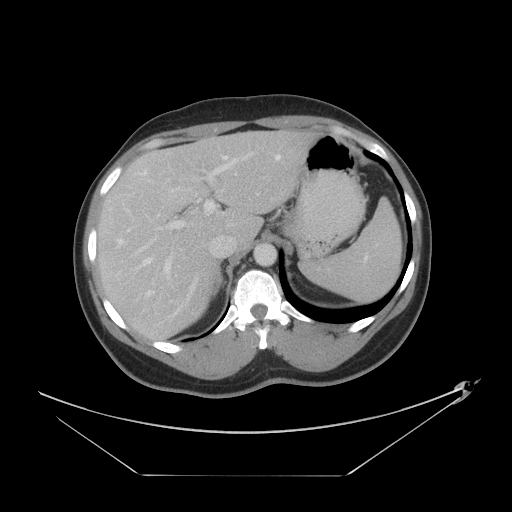
Contrast-enhanced abdominal CT, one axial slice. Position 29 of 44 along the scan axis. 120 kVp. Intravenous contrast given. Soft-tissue window (W 400 / L 40 HU). 512 × 512 image matrix, field of view 466 × 466 mm. Male patient, age 49 years. Case-level facts recorded for this patient, not image findings: diagnosis: colorectal cancer liver metastases, imaged before liver resection; multiple liver metastases: no; largest metastasis: 8.5 cm; disease in both lobes: yes.
Annotated regions visible in this slice (expert manual segmentation):
- hepatic veins: bounding box (x1, y1, x2, y2) in pixels: (143, 155, 281, 296)
- liver: (97, 131, 319, 341)
- planned liver remnant (the part of the liver to remain after resection): (158, 131, 320, 247)
- portal vein (with intrahepatic branches): (117, 160, 245, 274)